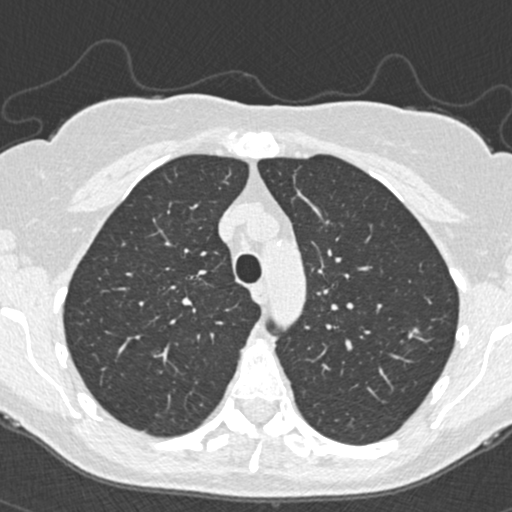
Low-dose screening chest CT, one axial slice. Slice 269 of 350 in the series (ordered by position). Reconstruction kernel B30f. Lung window (W 1500 / L -600 HU). 1 mm slice thickness. 512 × 512 image matrix, field of view 298 × 298 mm.
Outlined on this slice (outlined manually by an expert reader):
- lesion 1 (tumor, upper lobe of left lung): bounding box <408,328,419,339> (left, top, right, bottom; pixels)